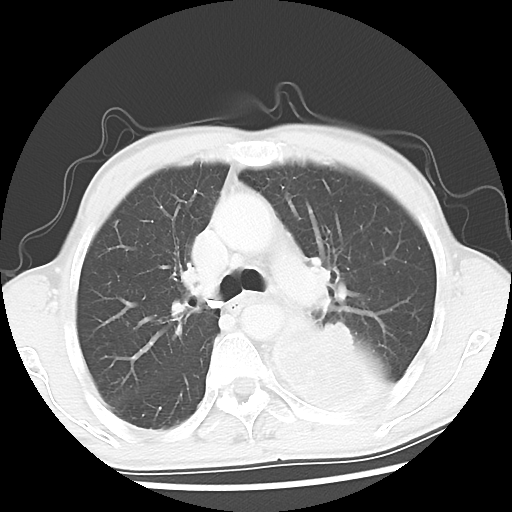
Chest CT, one axial slice. Slice 34 of 52 in the series (ordered by position). Lung window (W 1500 / L -600 HU). 5 mm slice thickness. 512 × 512 image matrix, field of view 318 × 318 mm. Male patient, age 60 years. Case-level facts recorded for this patient, not image findings: clinical TNM (as recorded): T4 N0 M0.
Annotated regions visible in this slice (bounding box drawn by a radiologist):
- lung tumour (recorded histology: squamous cell carcinoma): box from (x=269, y=311) to (x=393, y=423) px